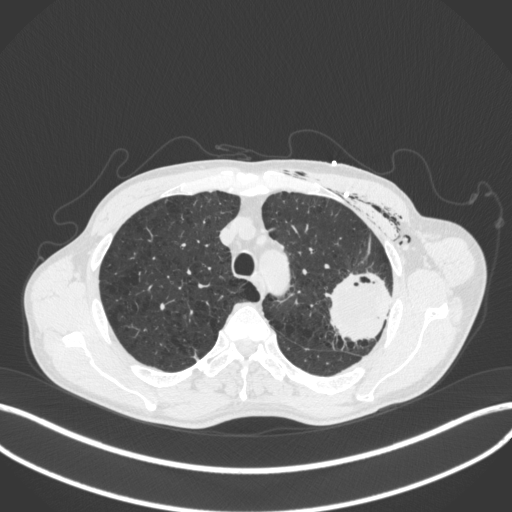
Chest CT, one axial slice. Slice 312 of 416 in the series (ordered by position). Reconstruction kernel B31f. 120 kVp. Lung window (W 1500 / L -600 HU). 1 mm slice thickness. 512 × 512 image matrix. Male patient, age 58 years. Case-level facts recorded for this patient, not image findings: clinical TNM (as recorded): T3 N0 M0.
Outlined on this slice (rectangle marked by the reading radiologist):
- lung tumour (recorded histology: adenocarcinoma): bounding box [x1, y1, x2, y2] px = [319, 271, 406, 349]